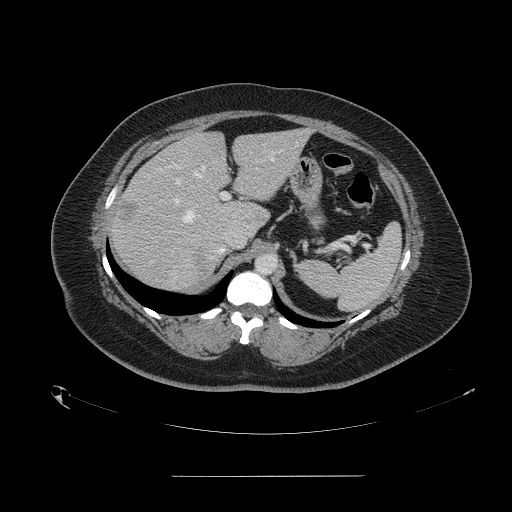
Contrast-enhanced abdominal CT, one axial slice. Position 103 of 164 along the scan axis. 120 kVp. Intravenous contrast given. Soft-tissue window (W 400 / L 40 HU). 2.5 mm slice thickness. 512 × 512 image matrix, field of view 495 × 495 mm. Female patient, age 52 years. From the clinical record (not read from this slice): diagnosis: colorectal cancer liver metastases, imaged before liver resection; multiple liver metastases: yes; largest metastasis: 3.5 cm; disease in both lobes: no.
Structures marked on this image (outlined manually by an expert reader):
- hepatic veins: bounding box [x1, y1, x2, y2] px = [182, 143, 297, 222]
- liver: [111, 130, 309, 291]
- planned liver remnant (the part of the liver to remain after resection): [174, 130, 309, 229]
- portal vein (with intrahepatic branches): [173, 177, 230, 205]
- liver metastasis: [194, 252, 207, 271]
- liver metastasis: [252, 213, 263, 223]
- liver metastasis: [119, 202, 138, 225]